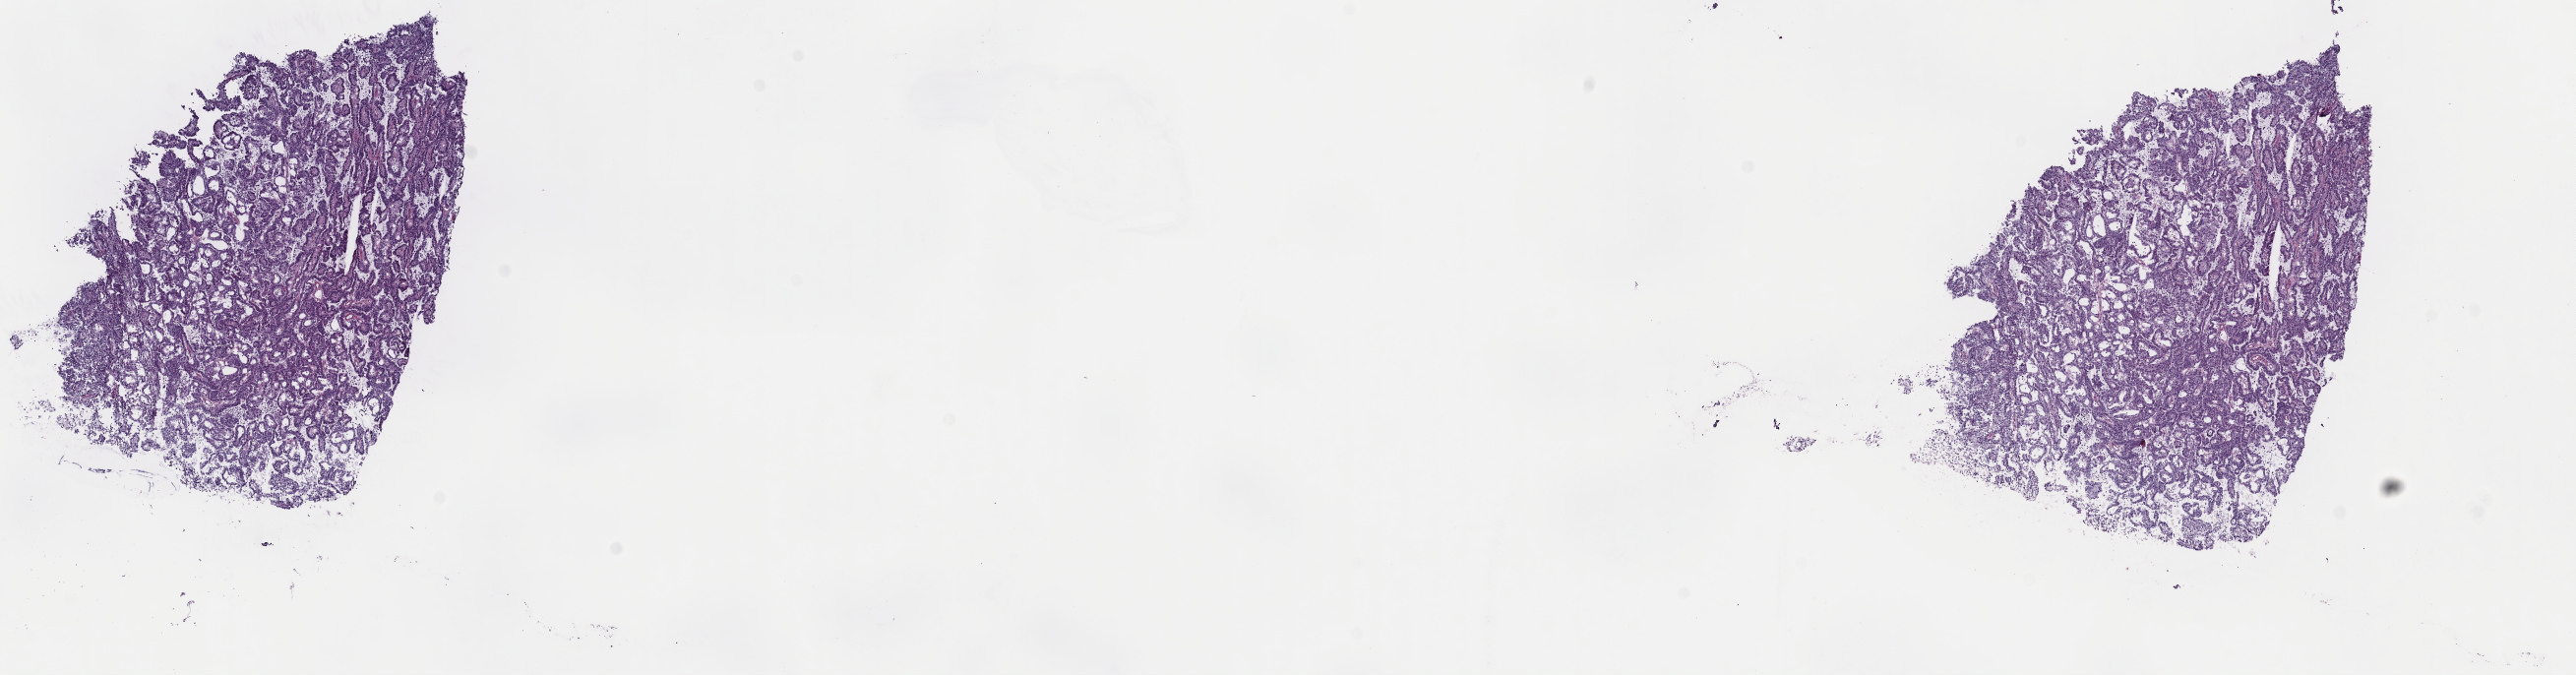
H&E whole-slide image, a low-resolution overview of the entire scanned area, about 20.7 x 5.4 mm. Frozen section from the top of the tissue portion. Sample: primary tumour, kidney. Male, age 75 years at initial diagnosis. Pathologist review of this section (percent, as recorded): tumour cells 100%, tumour nuclei 80%, normal cells 0%, stromal cells 0%, necrosis 0%. Inflammatory infiltration, as recorded: lymphocyte infiltration 3%, monocyte infiltration 2%, neutrophil infiltration 0%.
- TNM: T1b N1 MX
- AJCC pathologic stage: III (7th edition)
- diagnosis: Papillary adenocarcinoma, NOS